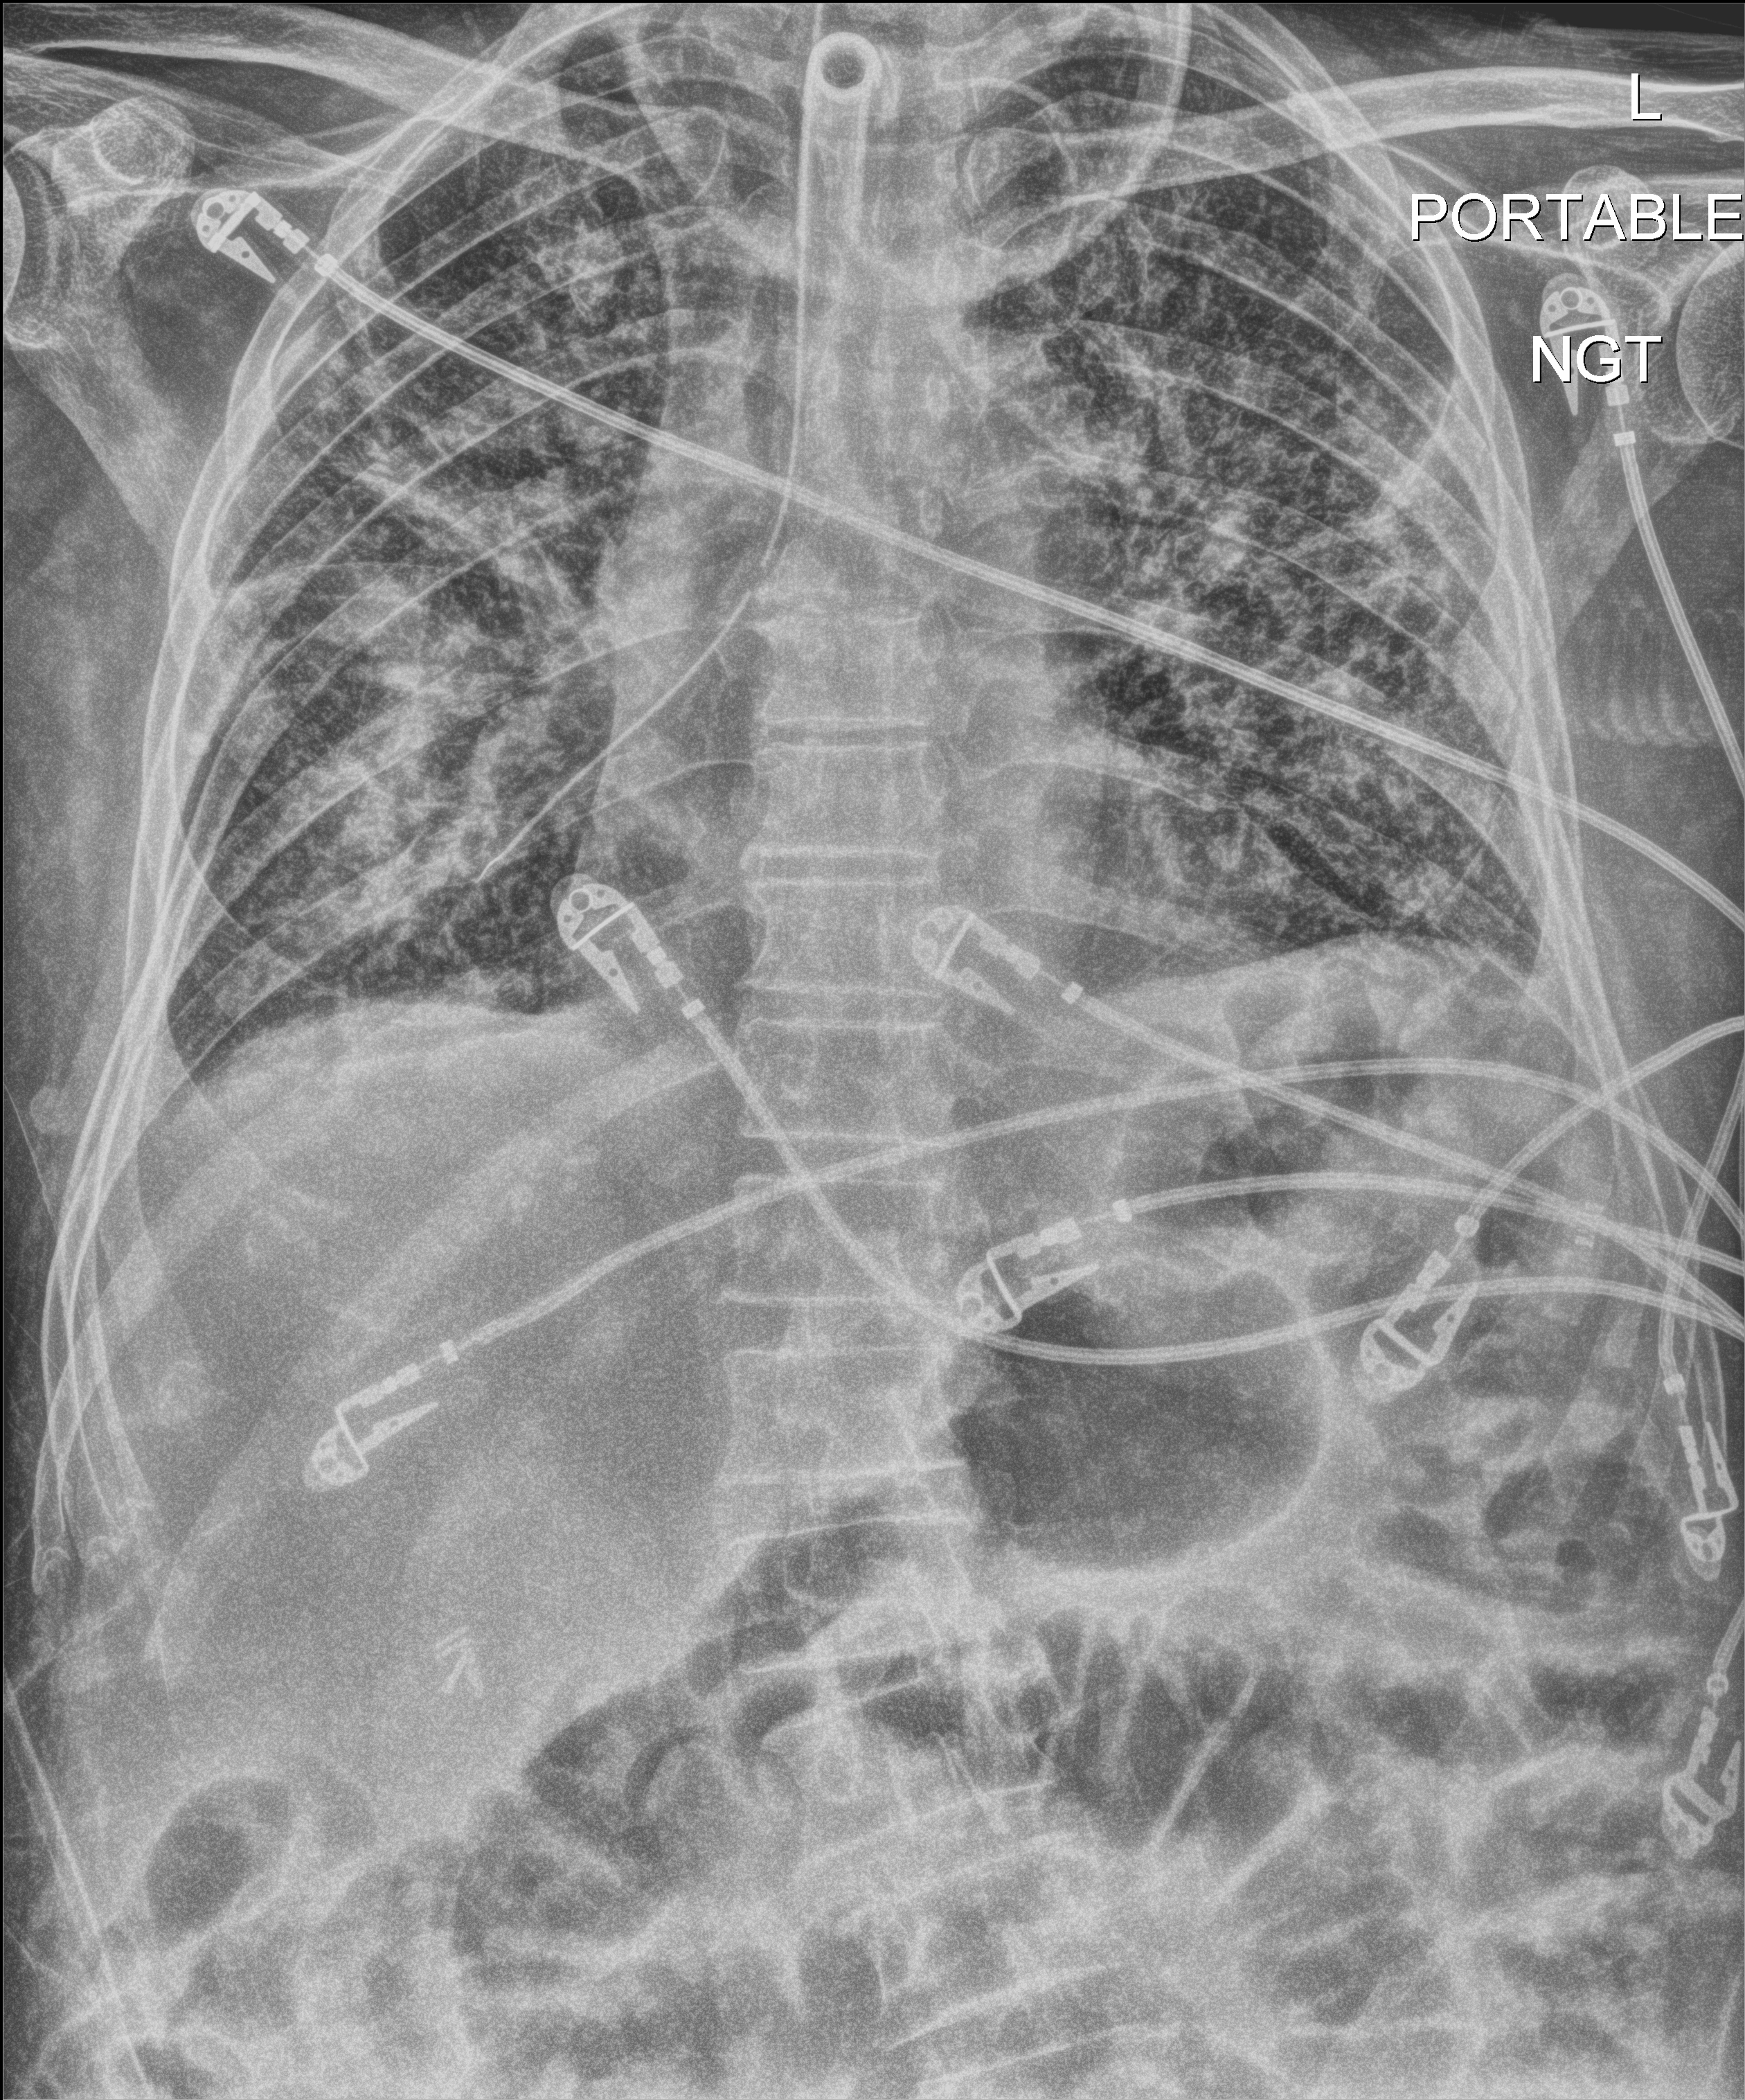
Chest radiograph (digital radiography); anteroposterior (AP) projection. Male patient hospitalised with COVID-19, age 75–90 years.
Hospital-stay facts (about this admission, not read from this image; timing relative to this image not recorded):
- COPD (admission record): no